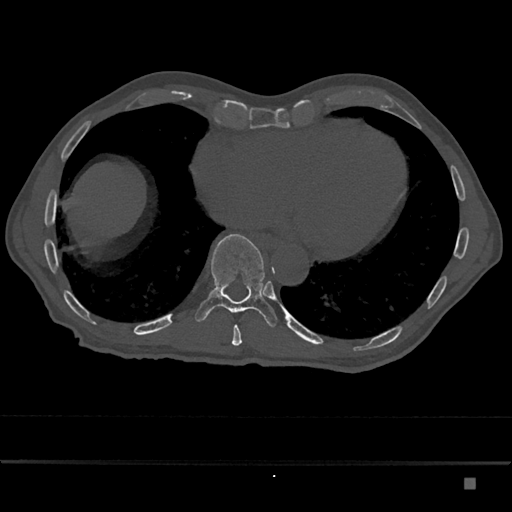
CT including the spine, one axial slice. Position 752 of 797 along the scan axis. Reconstruction kernel Br40s/3. 120 kVp. Bone window (W 1800 / L 400 HU). 512 × 512 image matrix, field of view 390 × 390 mm. Patient: male, 72 years. Case-level facts recorded for this patient, not image findings: primary cancer: prostate.
Outlined on this slice (semi-automatically segmented with operator editing):
- T10 vertebra: bounding box [x1, y1, x2, y2] px = [195, 234, 278, 327]
- T9 vertebra: [232, 325, 242, 346]